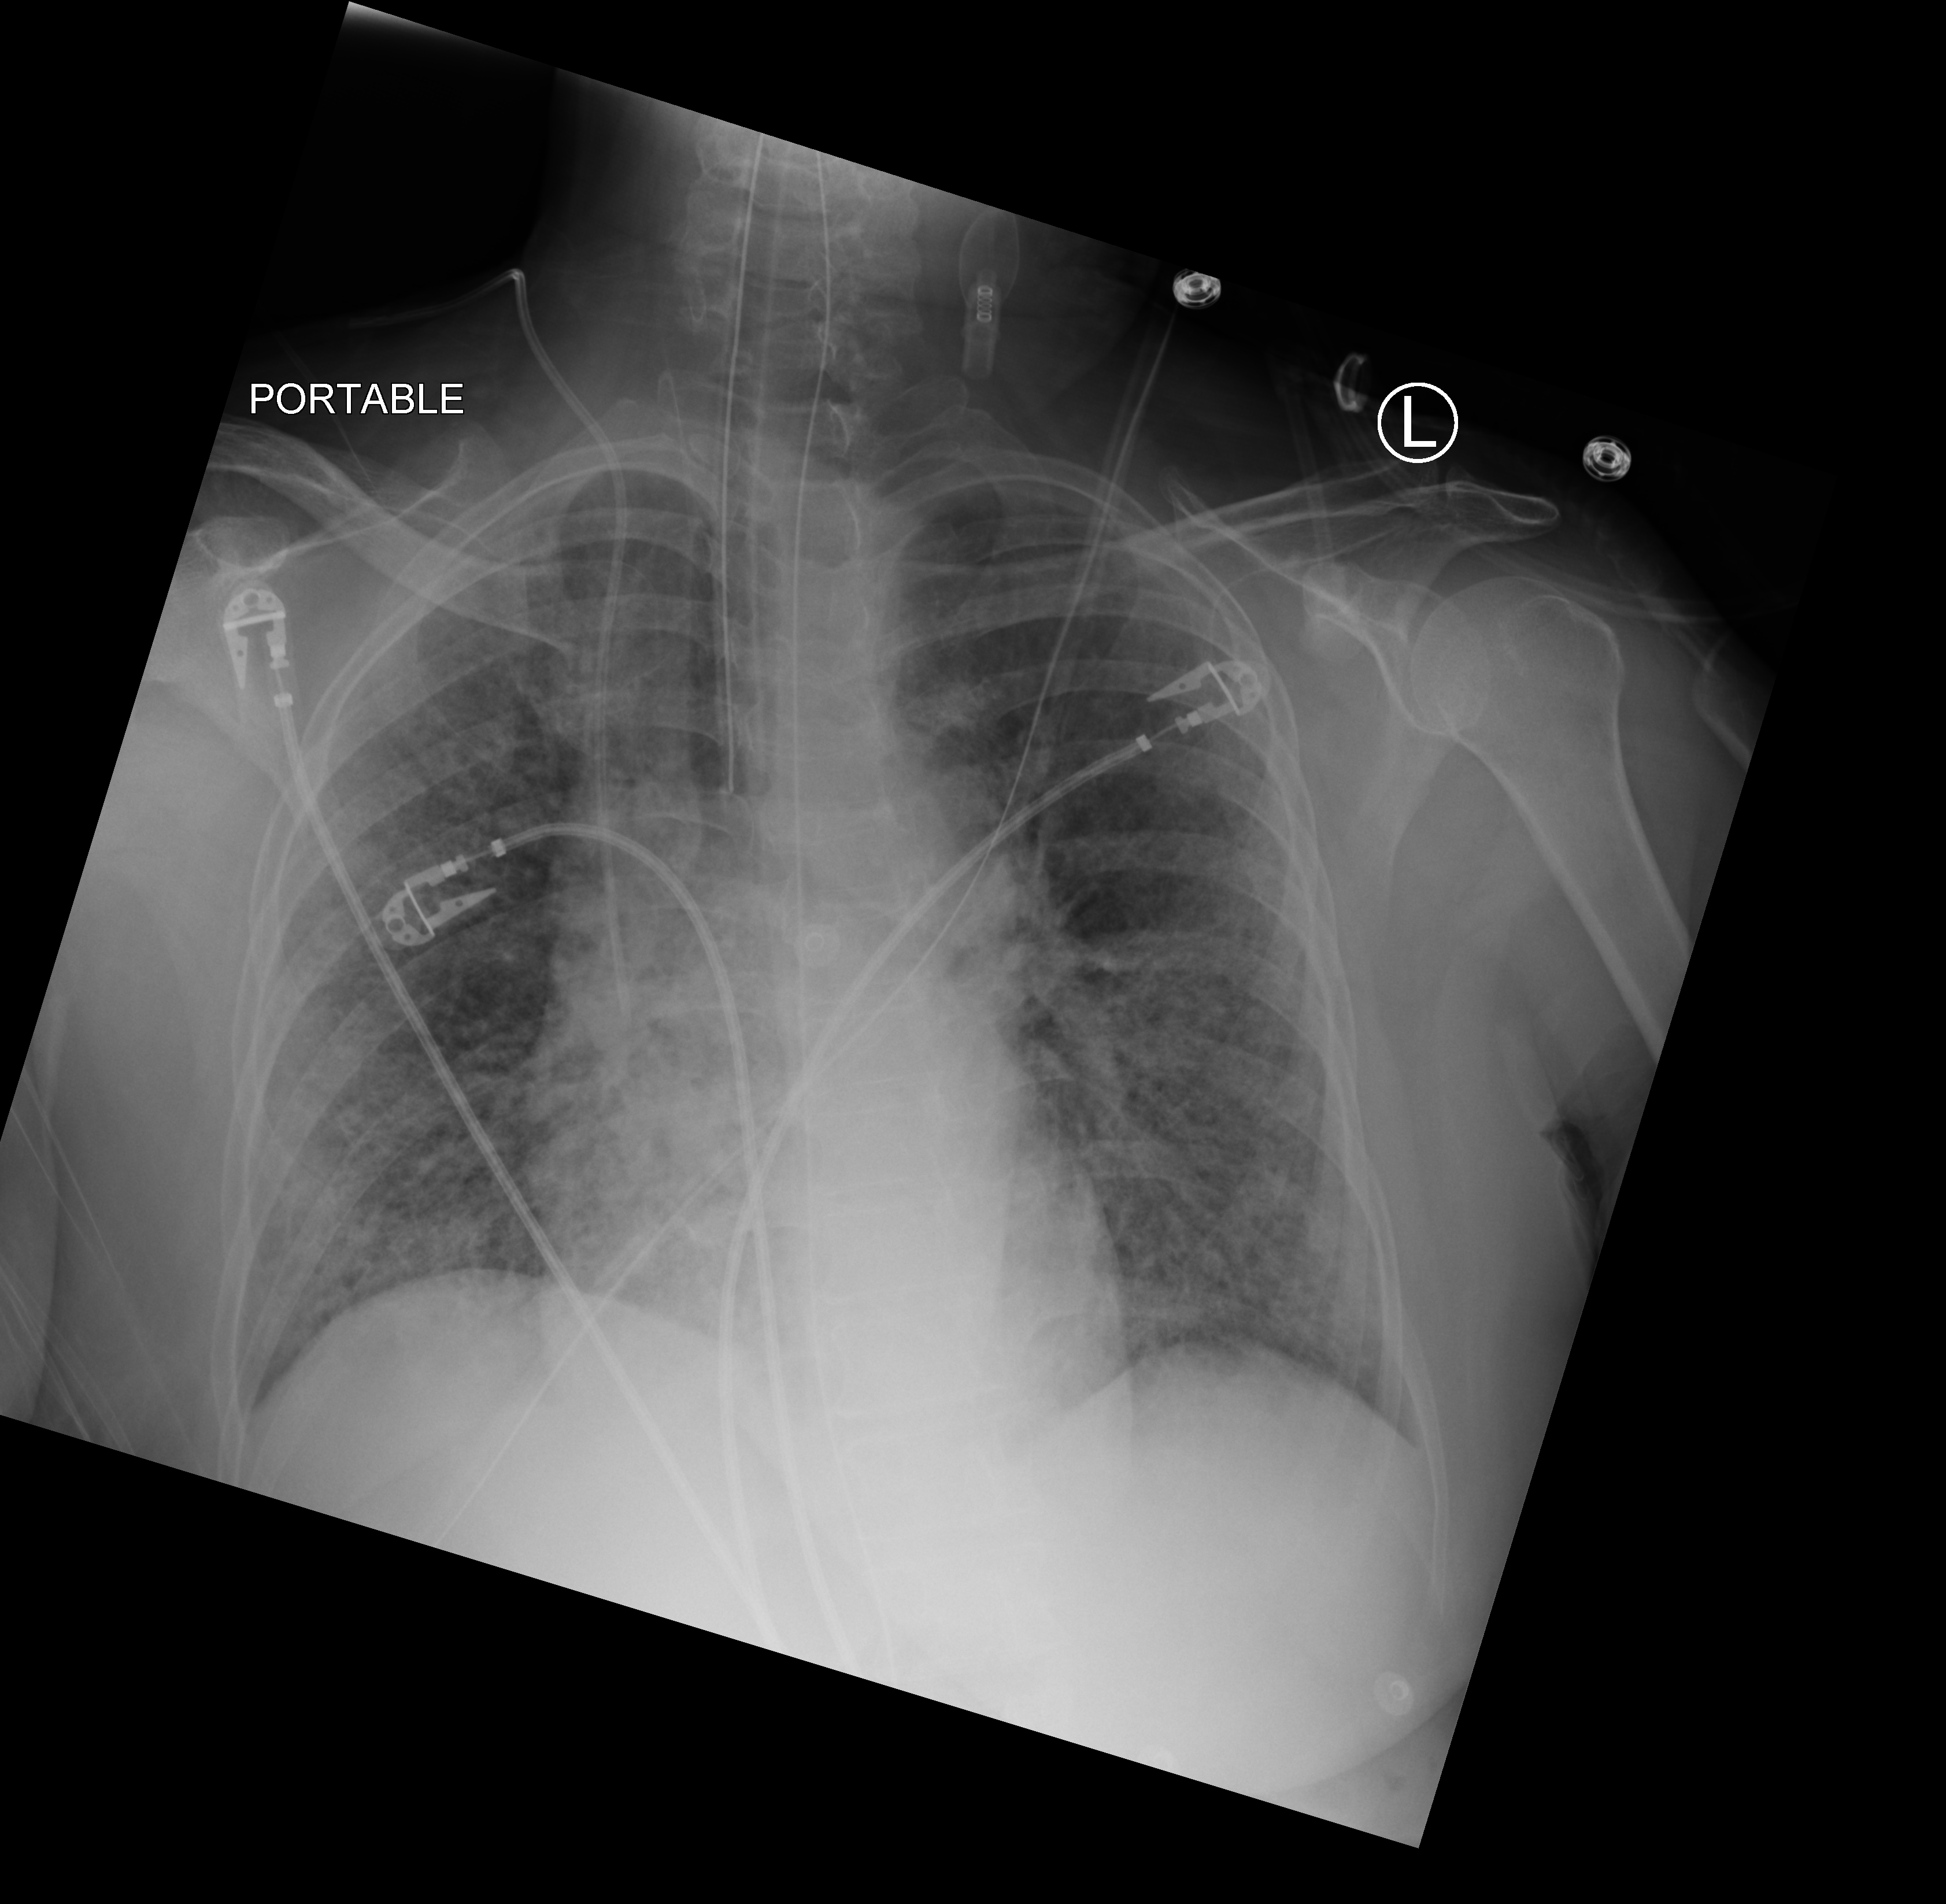
Bedside chest radiograph (computed radiography), anteroposterior (AP) projection. Female patient hospitalised with COVID-19, age 60–74 years.
From the hospital-stay record, not from the radiograph (when in the stay this image was taken is not recorded): mechanically ventilated during this hospital stay: yes; admitted to intensive care during this hospital stay: yes.